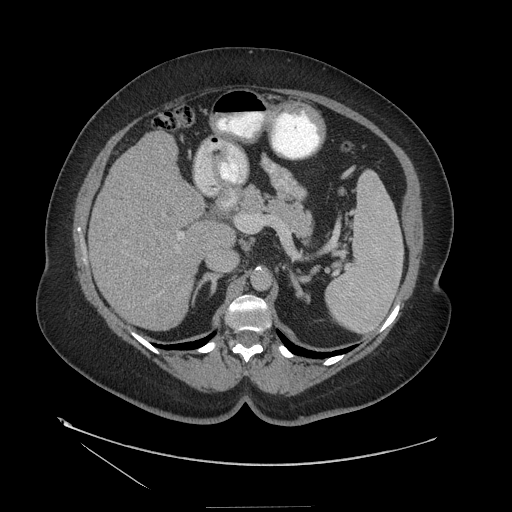
Contrast-enhanced abdominal CT (liver protocol), one axial slice. Position 69 of 127 along the scan axis. Reconstruction kernel STANDARD. 140 kVp. Soft-tissue window (W 400 / L 40 HU). 2.5 mm slice thickness. 512 × 512 image matrix, field of view 480 × 480 mm. Case-level facts recorded for this patient, not image findings: diagnosis: hepatocellular carcinoma (patient treated with transarterial chemoembolisation; whether this scan precedes or follows treatment is not stated here); TNM stage (as recorded): Stage-II; Child-Pugh class: A; tumour size: 3 cm.
Annotated regions visible in this slice (semi-automatic segmentation, software-assisted and operator-edited):
- liver parenchyma outside the tumour (the mass and vessels are separate outlines, so this box may not span the whole liver): bounding box [x1, y1, x2, y2] px = [90, 132, 212, 330]
- liver vessels: [178, 233, 184, 239]